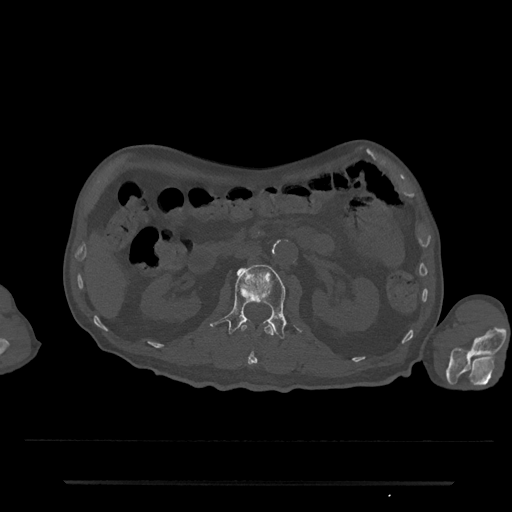
CT including the spine, one axial slice; position 81 of 797 along the scan axis; 120 kVp; bone window (W 1800 / L 400 HU); 0.5 mm slice thickness; 512 × 512 image matrix, field of view 427 × 427 mm. Male patient, age 74 years. Case-level facts recorded for this patient, not image findings: primary cancer: prostate.
Annotated regions visible in this slice (semi-automatically segmented with operator editing):
- L1 vertebra: bounding box (x1, y1, x2, y2) in pixels: (240, 323, 275, 367)
- L2 vertebra: (210, 264, 286, 340)